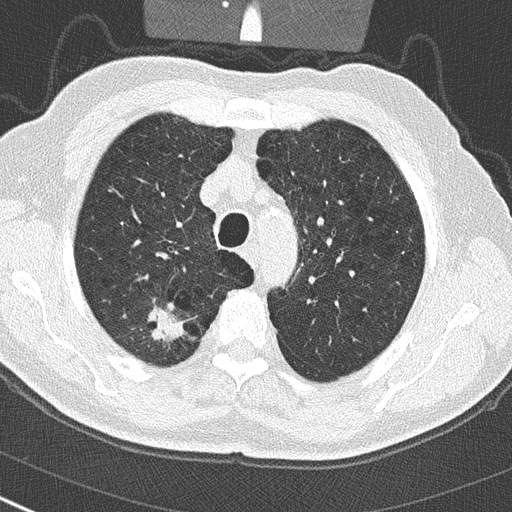
Low-dose screening chest CT, one axial slice. Position 224 of 290 along the scan axis. Reconstruction kernel B50f. Lung window (W 1500 / L -600 HU). 2 mm slice thickness. 512 × 512 image matrix, field of view 300 × 300 mm.
Structures marked on this image (manually delineated by an expert):
- lesion 1 (tumor, upper lobe of right lung): bounding box [x1, y1, x2, y2] px = [140, 307, 186, 348]